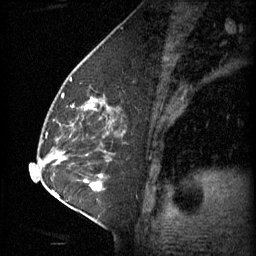
Breast MRI (dynamic contrast-enhanced), one sagittal slice; position 31 of 60 along the scan axis; 3 images stored at this slice position (order not interpretable as contrast timing); 1.5 T; TE 4.2 ms, TR 11 ms; 2 mm slice thickness; 256 × 256 image matrix, field of view 180 × 180 mm. Female patient, age 62 years.
Annotated regions visible in this slice (semi-automatically segmented with operator editing):
- analysis volume of interest (the breast-tissue region the enhancement analysis was run in; not a lesion): bounding box (x1, y1, x2, y2) in pixels: (55, 72, 120, 127)
- tumour enhancement mask (voxels above the 70 % enhancement threshold inside the analysis volume of interest): (87, 98, 94, 109)